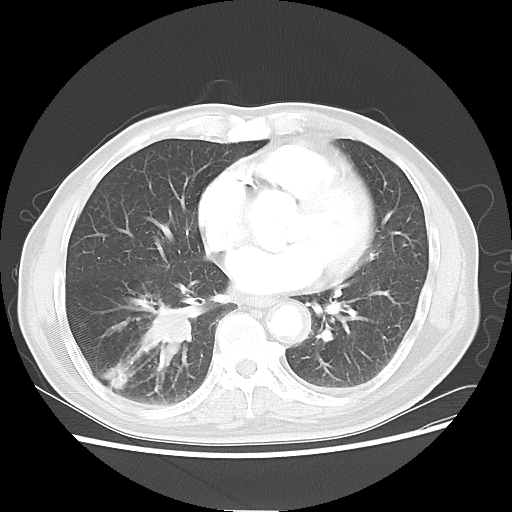
Chest CT, one axial slice; slice 25 of 58 in the series (ordered by position); reconstruction kernel LUNG; 120 kVp; lung window (W 1500 / L -600 HU); 512 × 512 image matrix, field of view 360 × 360 mm. Male patient, age 74 years. Case-level facts recorded for this patient, not image findings: clinical TNM (as recorded): T1c N1 M1.
Outlined on this slice (rectangle marked by the reading radiologist):
- lung tumour (recorded histology: adenocarcinoma): bounding box [x1, y1, x2, y2] px = [130, 295, 201, 370]